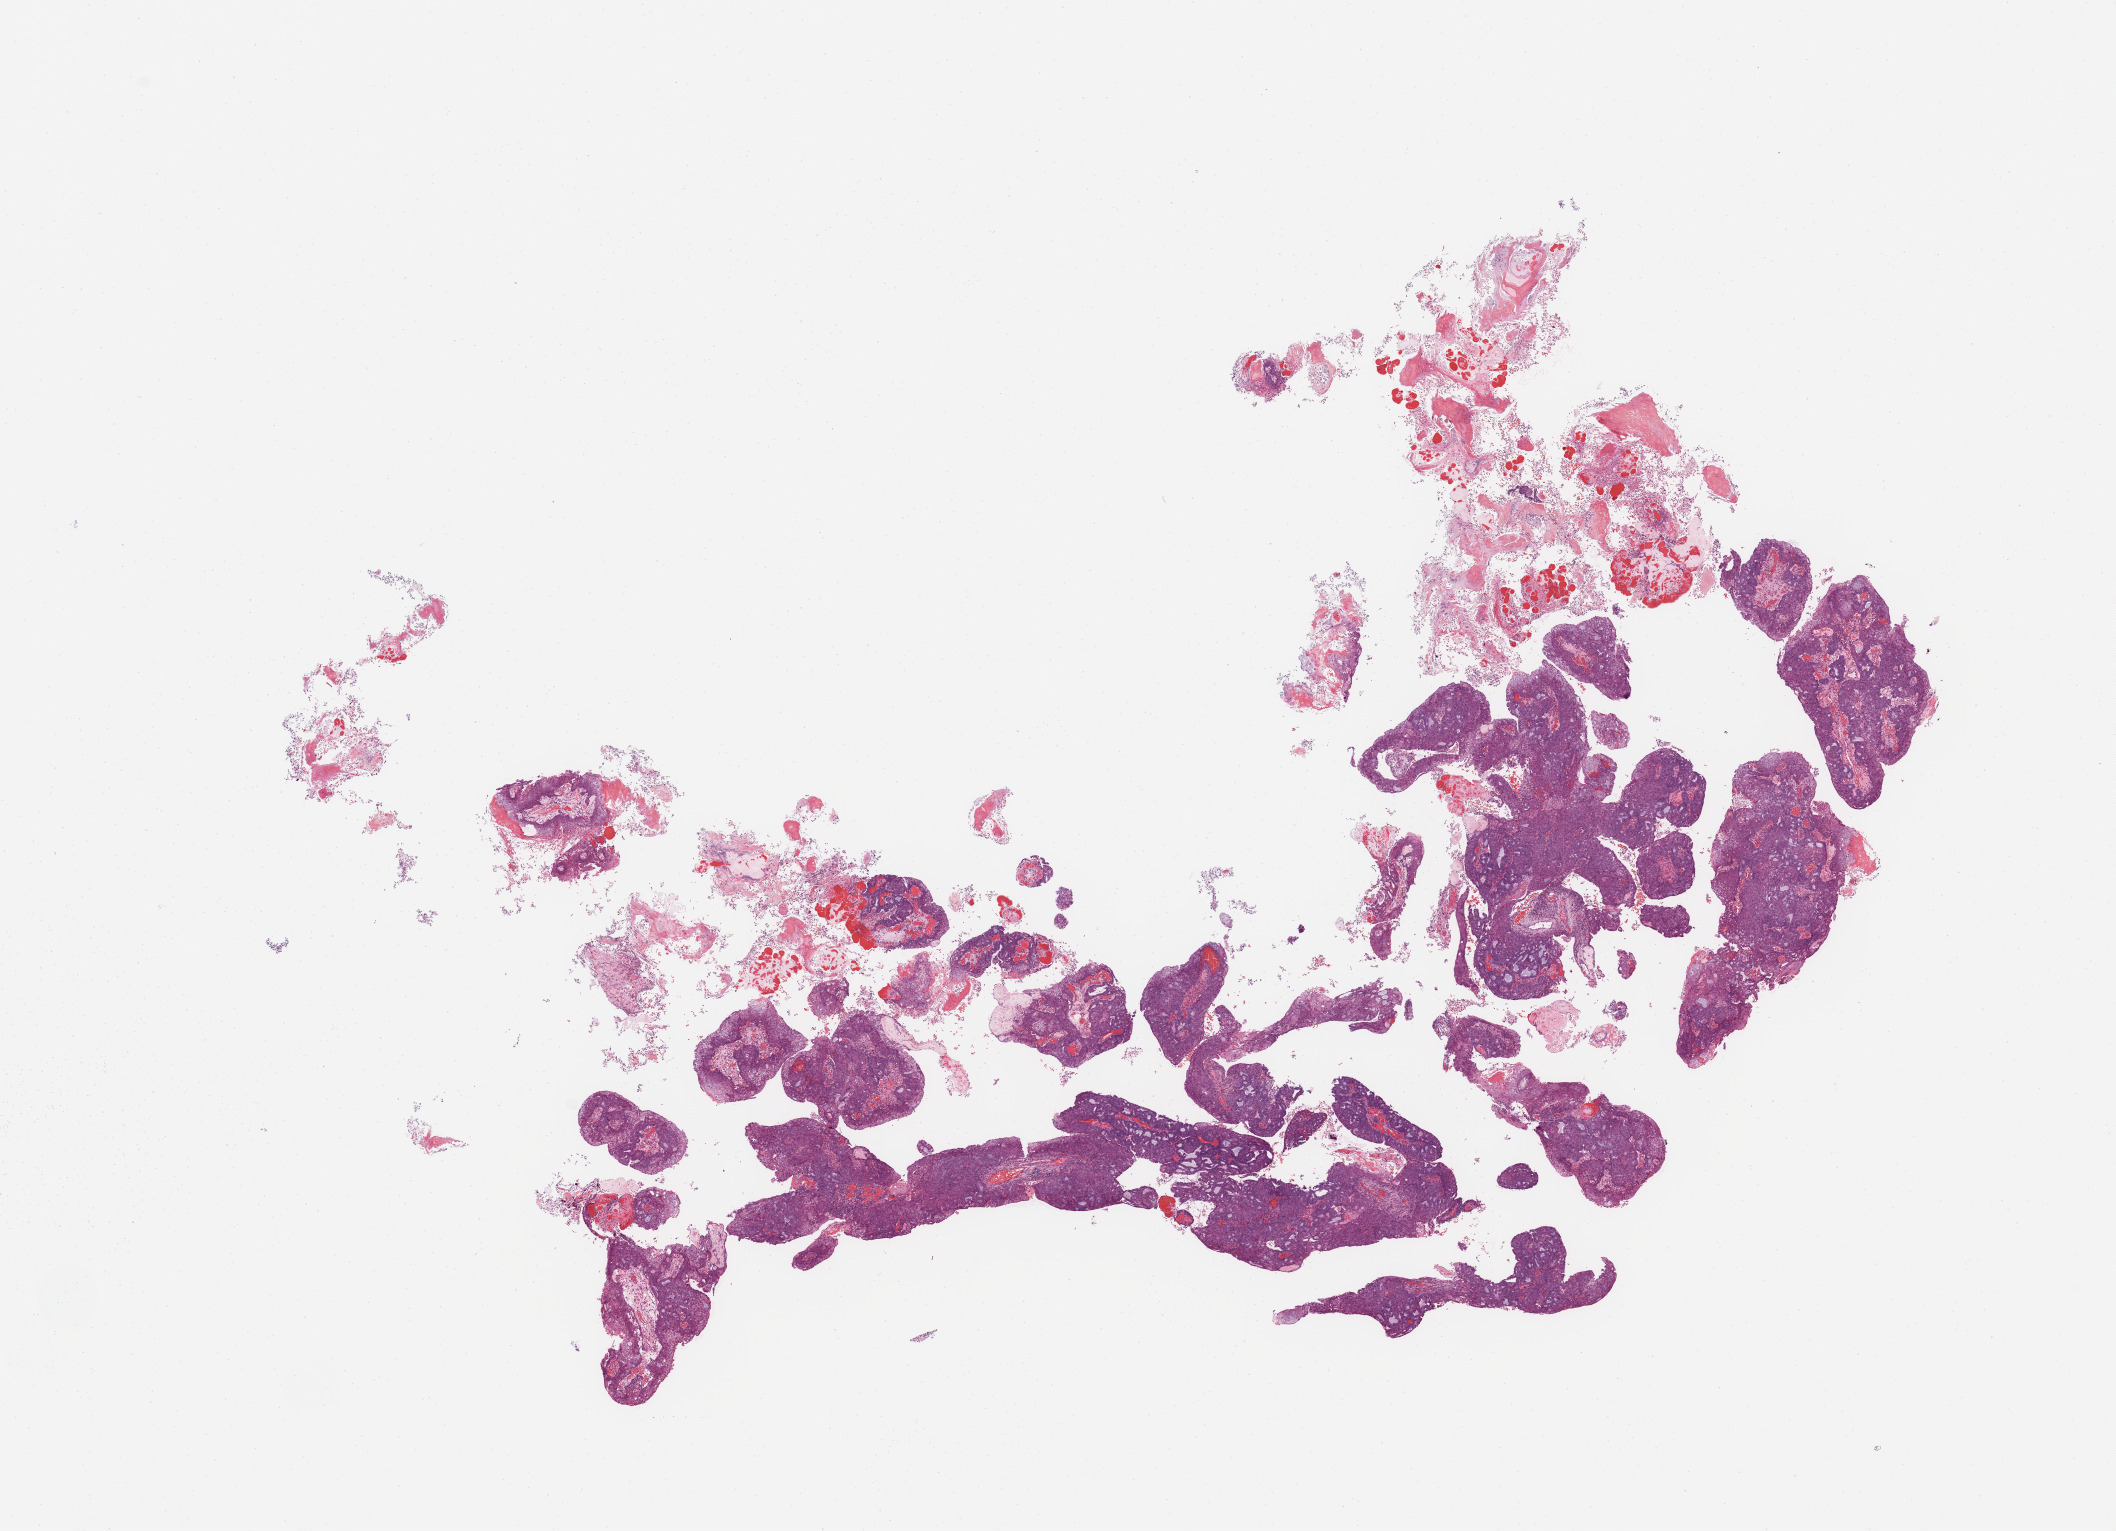
Digitized H&E-stained tissue section (whole slide), whole scanned area (about 16.7 x 12.1 mm) shown as a low-resolution overview, tumour tissue sample, sampled site: uterus. Patient: female, age 60 years. Composition of this section per pathologist review: tumour nuclei 95%, necrosis 0%.
Diagnosis: Endometrioid adenocarcinoma, NOS.